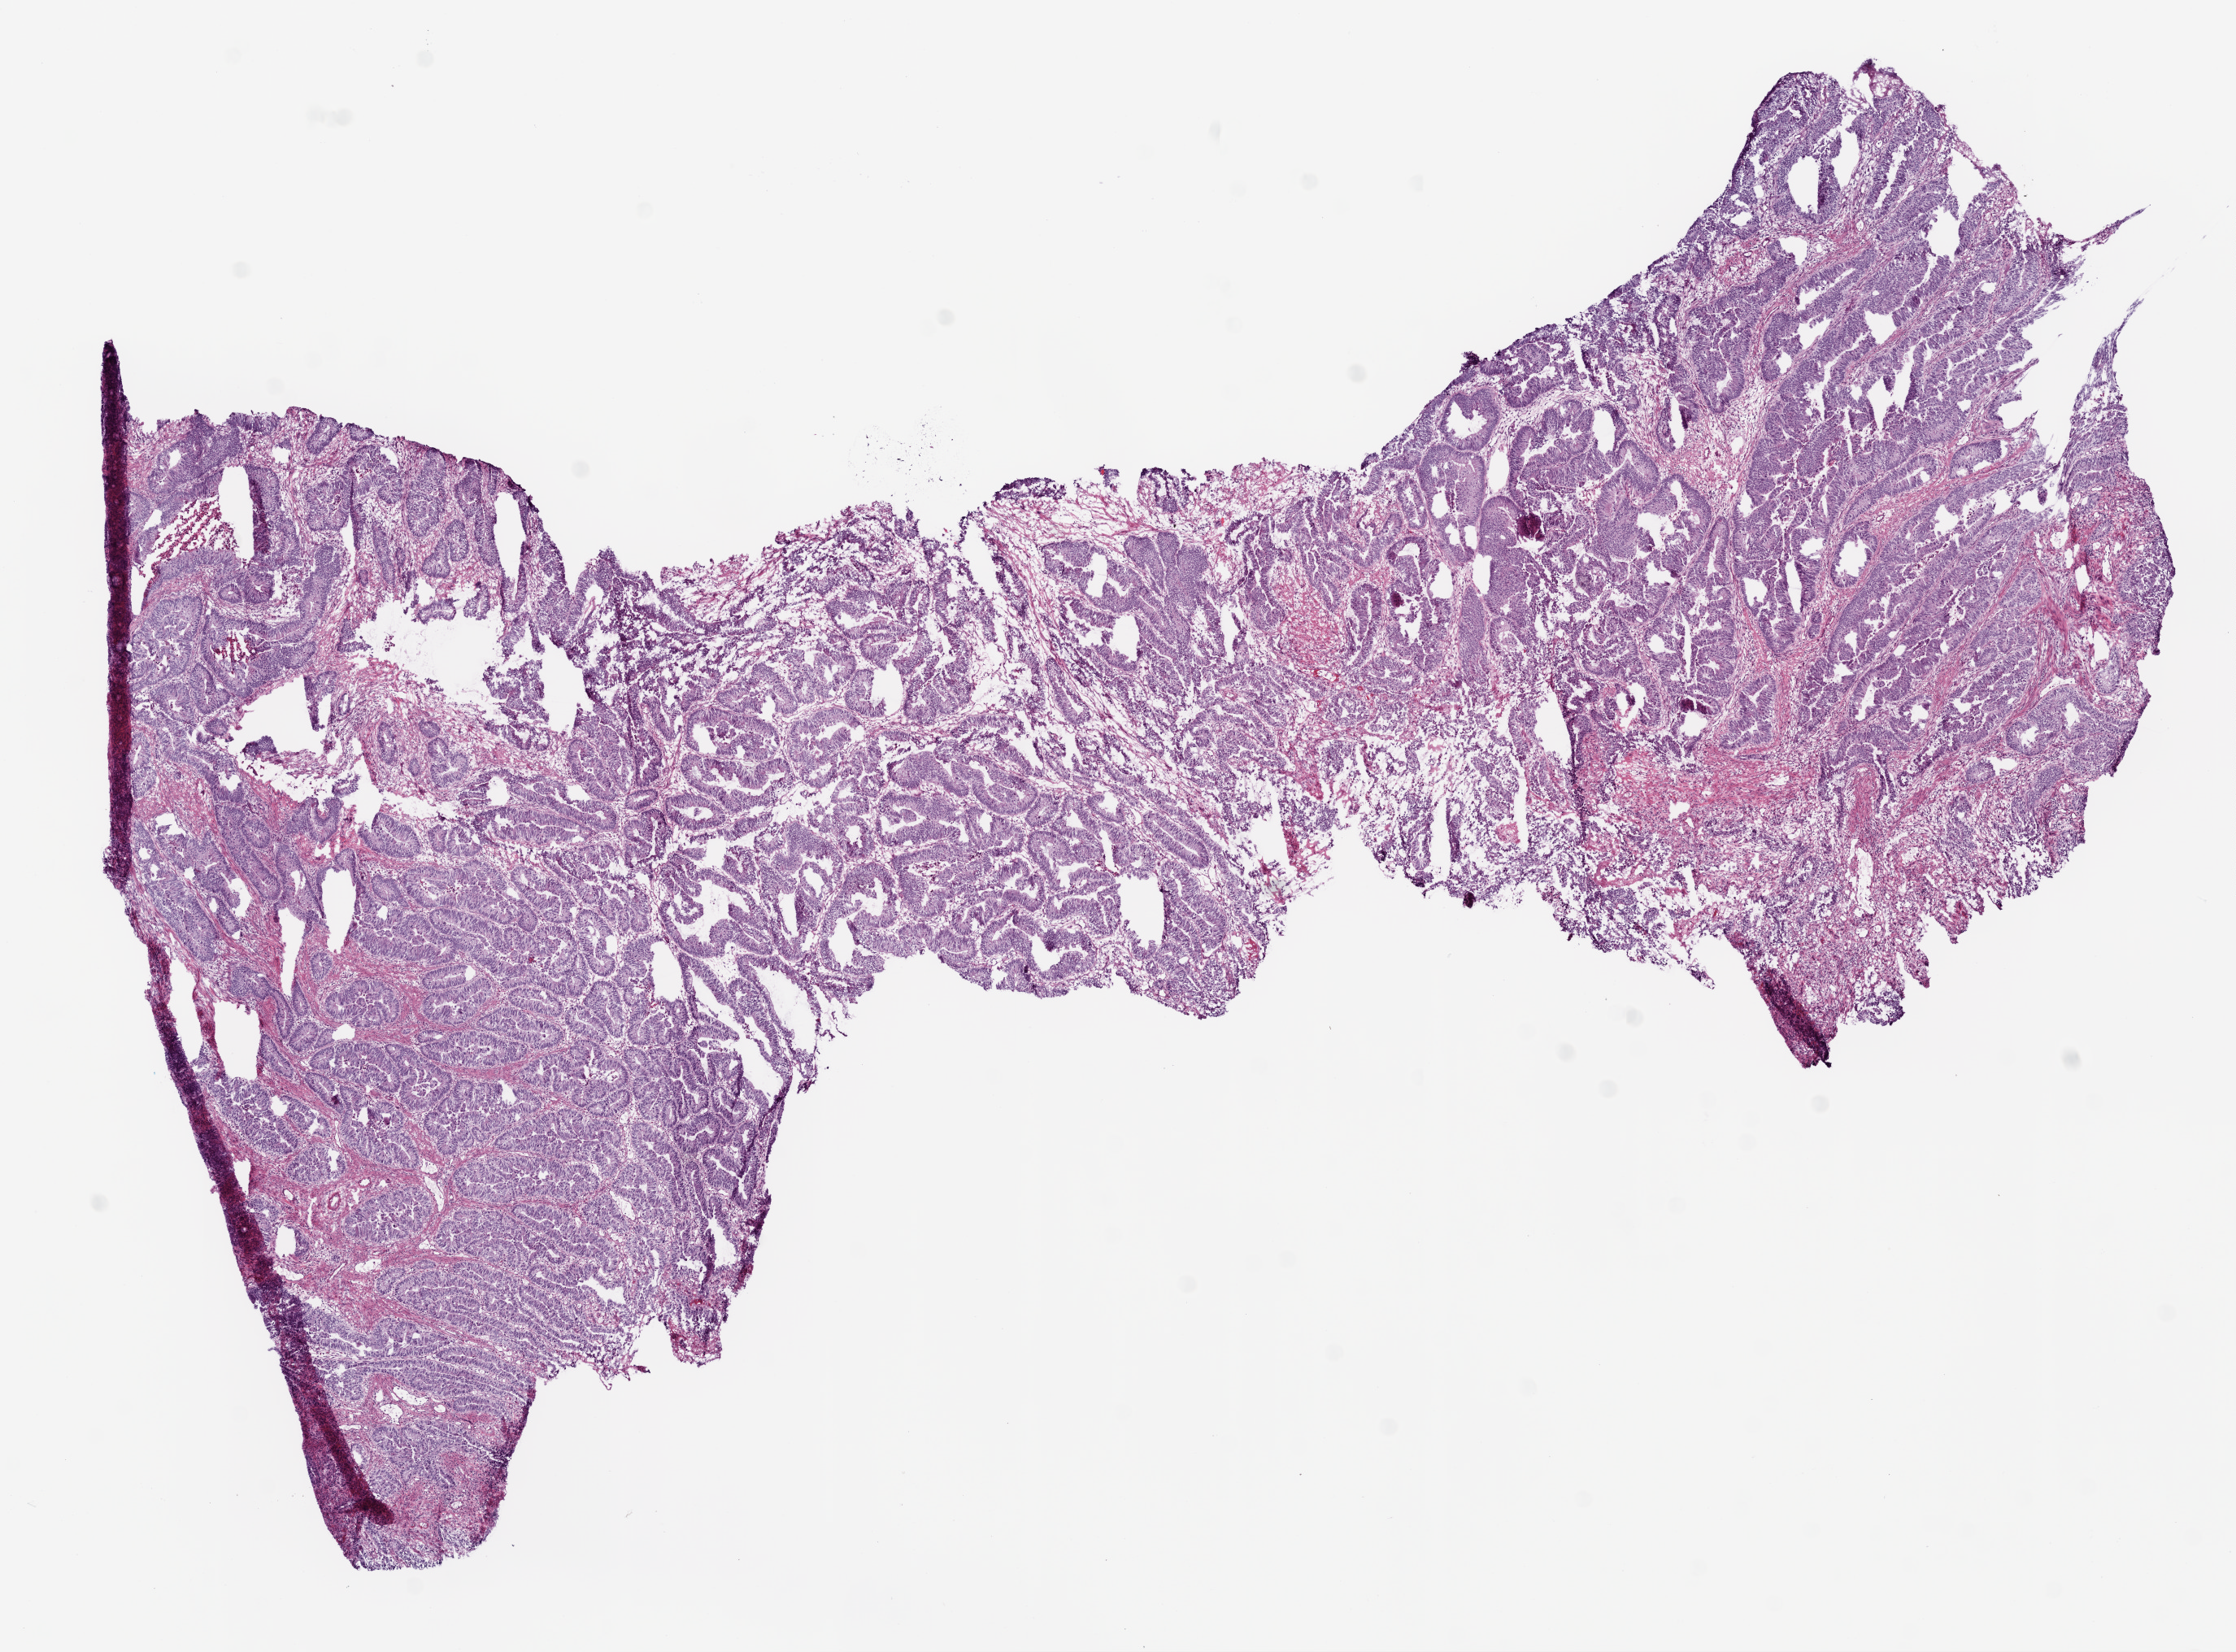
Digitized H&E-stained tissue section (whole slide), whole scanned area (about 11.0 x 8.2 mm, acquisition: 20x scan) shown as a low-resolution overview. Frozen section from the top of the tissue portion. Sample: primary tumour, colon. Female, age 63 years at initial diagnosis. Pathologist review of this section (percent, as recorded): tumour cells 78%, tumour nuclei 80%, normal cells 0%, stromal cells 20%, necrosis 2%.
* lymph nodes positive (case pathology): 6 of 33 examined
* diagnosis: Adenocarcinoma, NOS (cecum)
* AJCC pathologic stage: IV (6th edition)